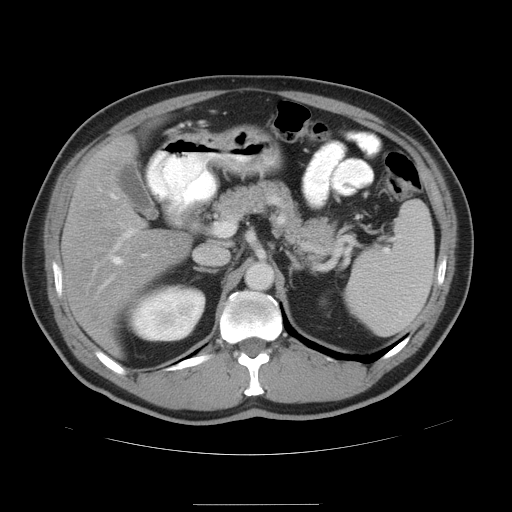
Contrast-enhanced abdominal CT, one axial slice; position 27 of 47 along the scan axis; 120 kVp; intravenous contrast given; soft-tissue window (W 400 / L 40 HU); 512 × 512 image matrix, field of view 420 × 420 mm. Male patient, age 61 years. Case-level facts recorded for this patient, not image findings: diagnosis: colorectal cancer liver metastases, imaged before liver resection; multiple liver metastases: no; largest metastasis: 1.2 cm; chemotherapy before resection: yes.
Annotated regions visible in this slice (expert manual segmentation):
- hepatic veins: bounding box [x1, y1, x2, y2] px = [106, 194, 122, 284]
- liver: [63, 137, 191, 355]
- planned liver remnant (the part of the liver to remain after resection): [65, 138, 191, 355]
- portal vein (with intrahepatic branches): [116, 222, 218, 248]